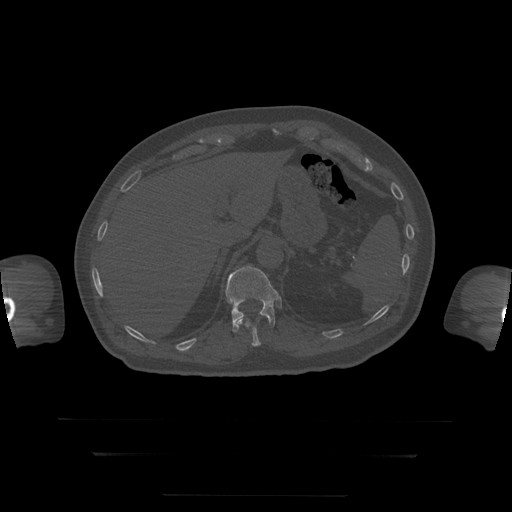
CT including the spine, one axial slice. Slice 85 of 397 in the series (ordered by position). Reconstruction kernel STANDARD. Bone window (W 1800 / L 400 HU). 1.25 mm slice thickness. 512 × 512 image matrix, field of view 510 × 510 mm. Patient age 73 years. From the clinical record (not read from this slice): primary cancer: prostate.
Structures marked on this image (semi-automatic segmentation, software-assisted and operator-edited):
- T11 vertebra: bounding box [x1, y1, x2, y2] px = [237, 318, 275, 347]
- T12 vertebra: [226, 266, 281, 333]